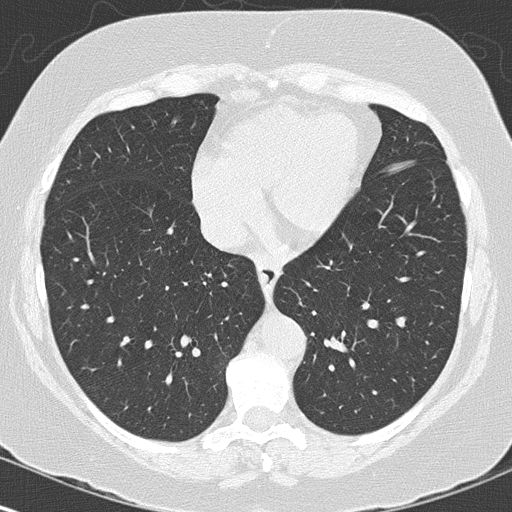
Low-dose screening chest CT, one axial slice; position 51 of 144 along the scan axis; reconstruction kernel B50f; 120 kVp; lung window (W 1500 / L -600 HU); 2 mm slice thickness; 512 × 512 image matrix, field of view 316 × 316 mm.
Structures marked on this image (expert manual segmentation):
- lesion 1 (tumor, lower lobe of left lung): bounding box (x1, y1, x2, y2) in pixels: (362, 297, 370, 310)